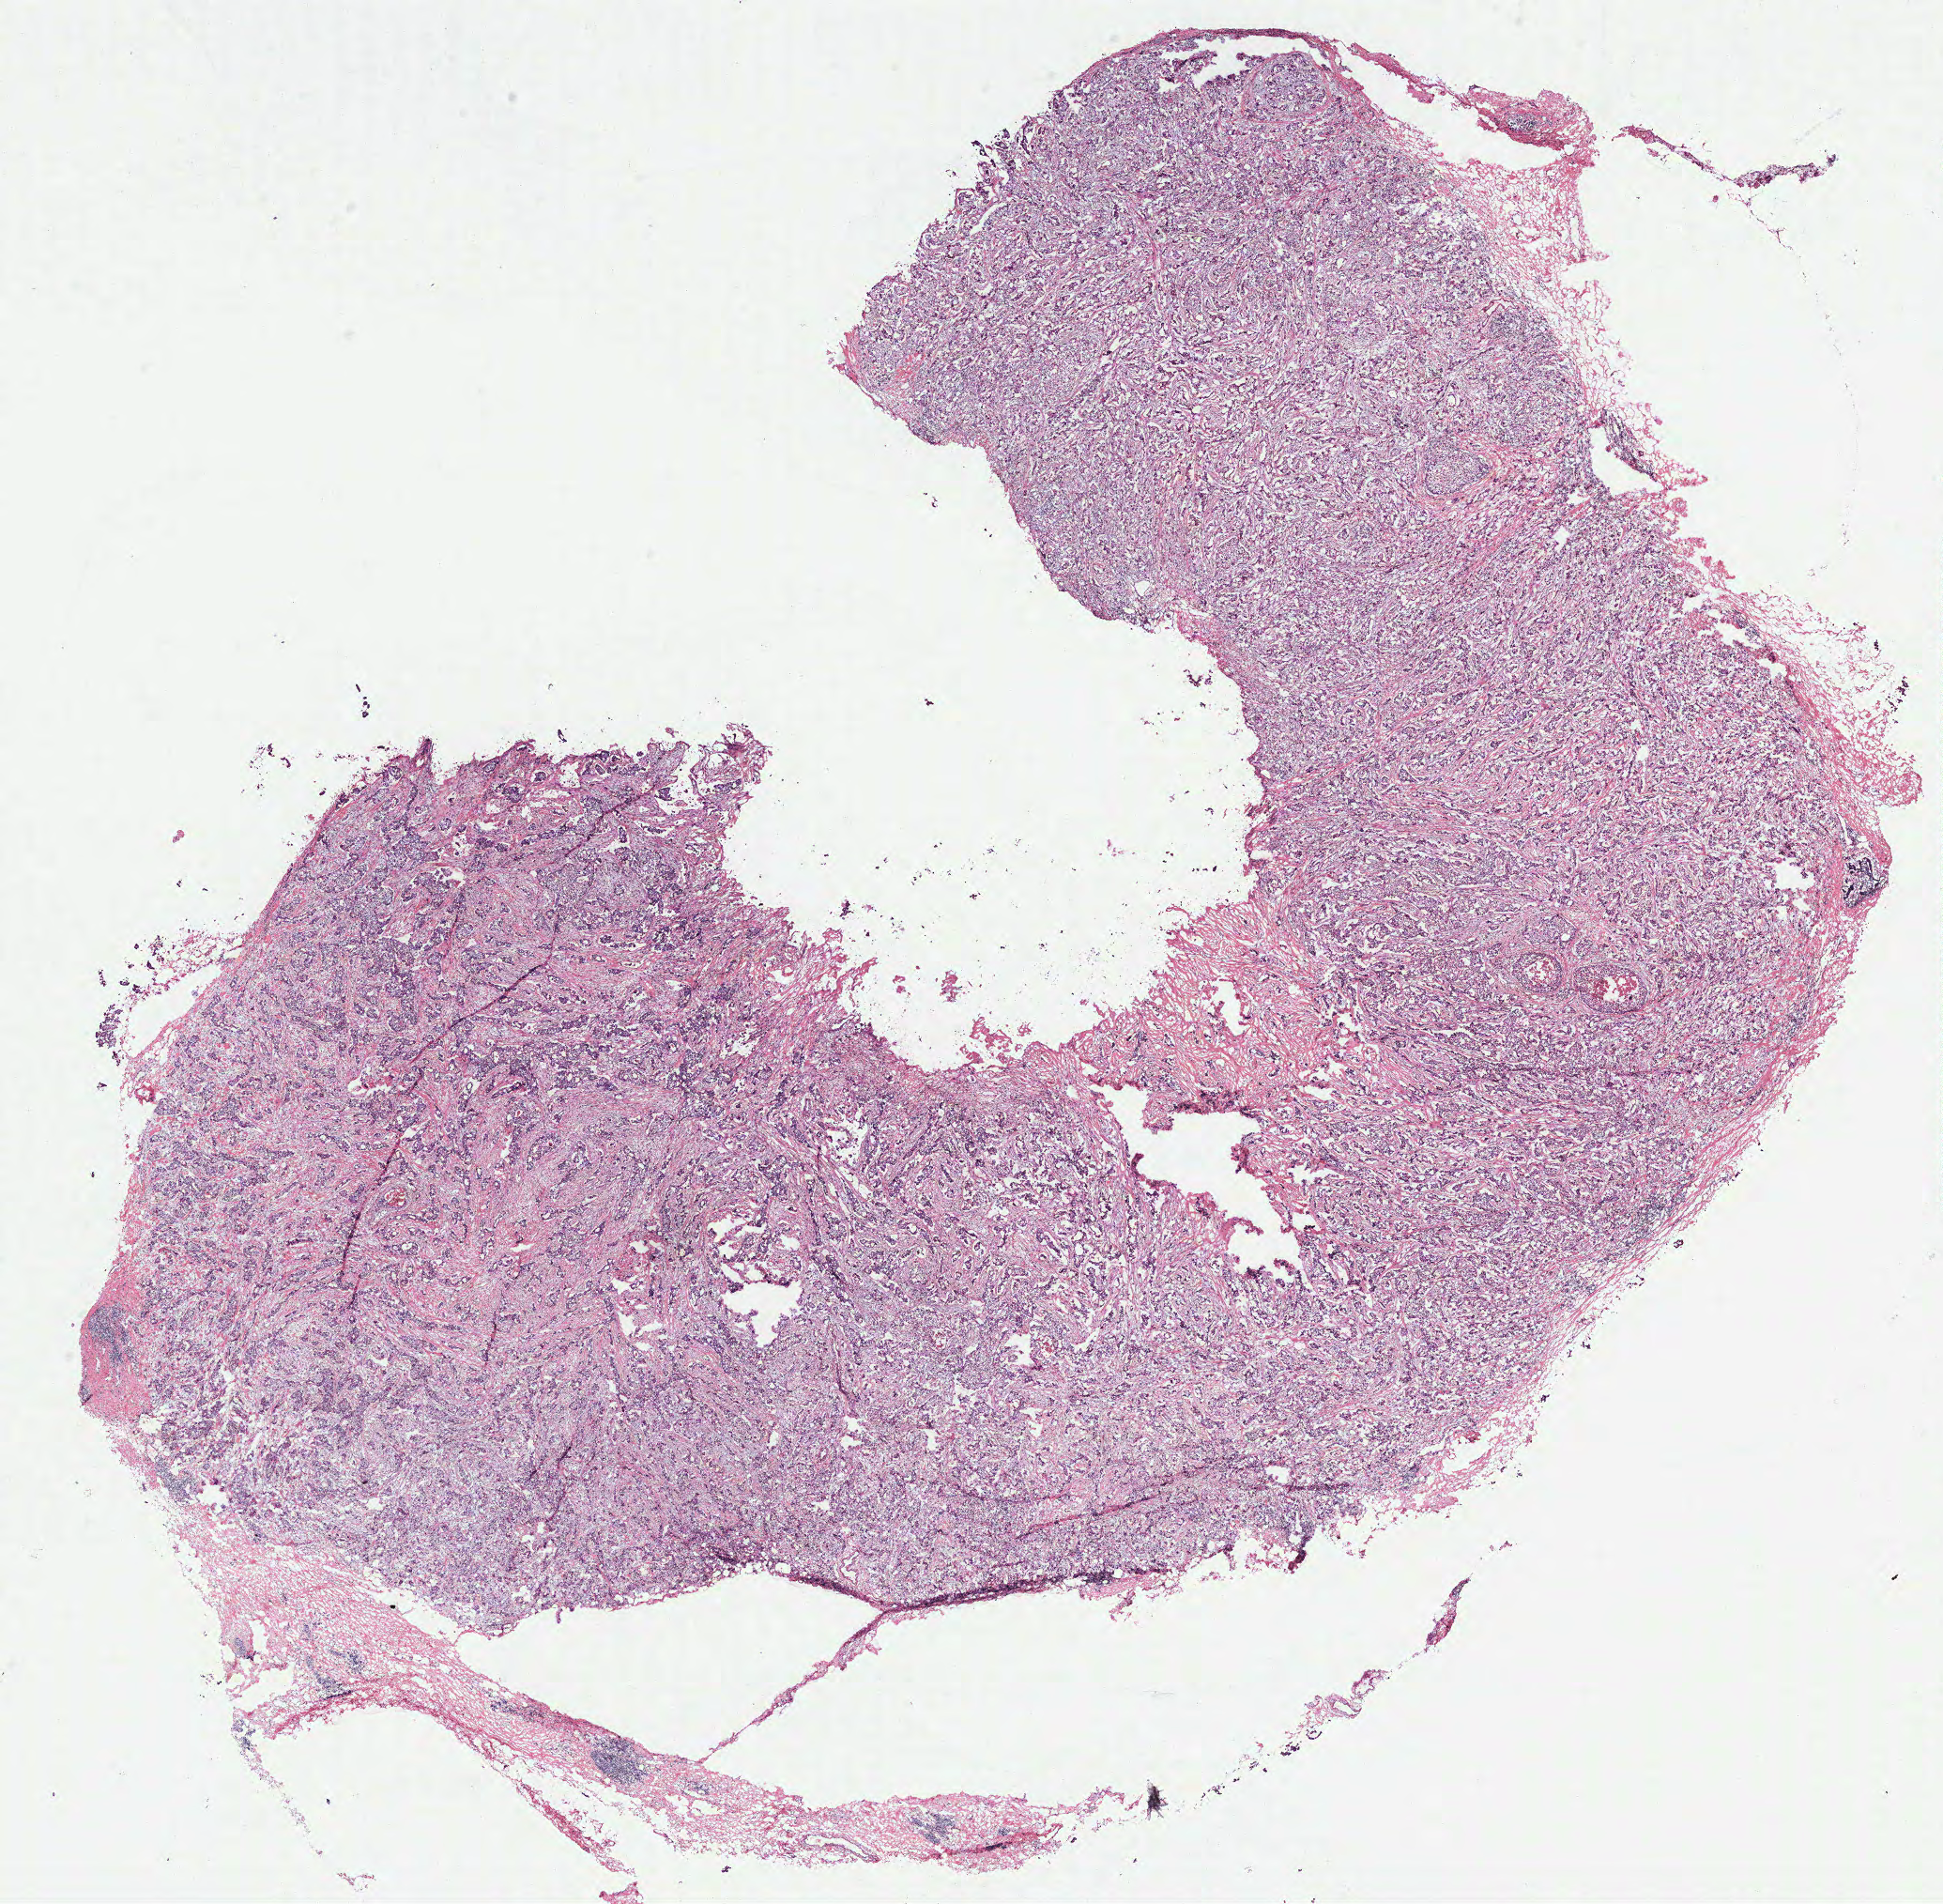
Digitized Hematoxylin and eosin (H&E) stained tissue section (whole slide) — low-resolution overview of the scanned area, about 16.6 x 16.2 mm; breast, tissue type not recorded. 50-year-old female patient.
• patient diagnosis: Infiltrating duct carcinoma, NOS